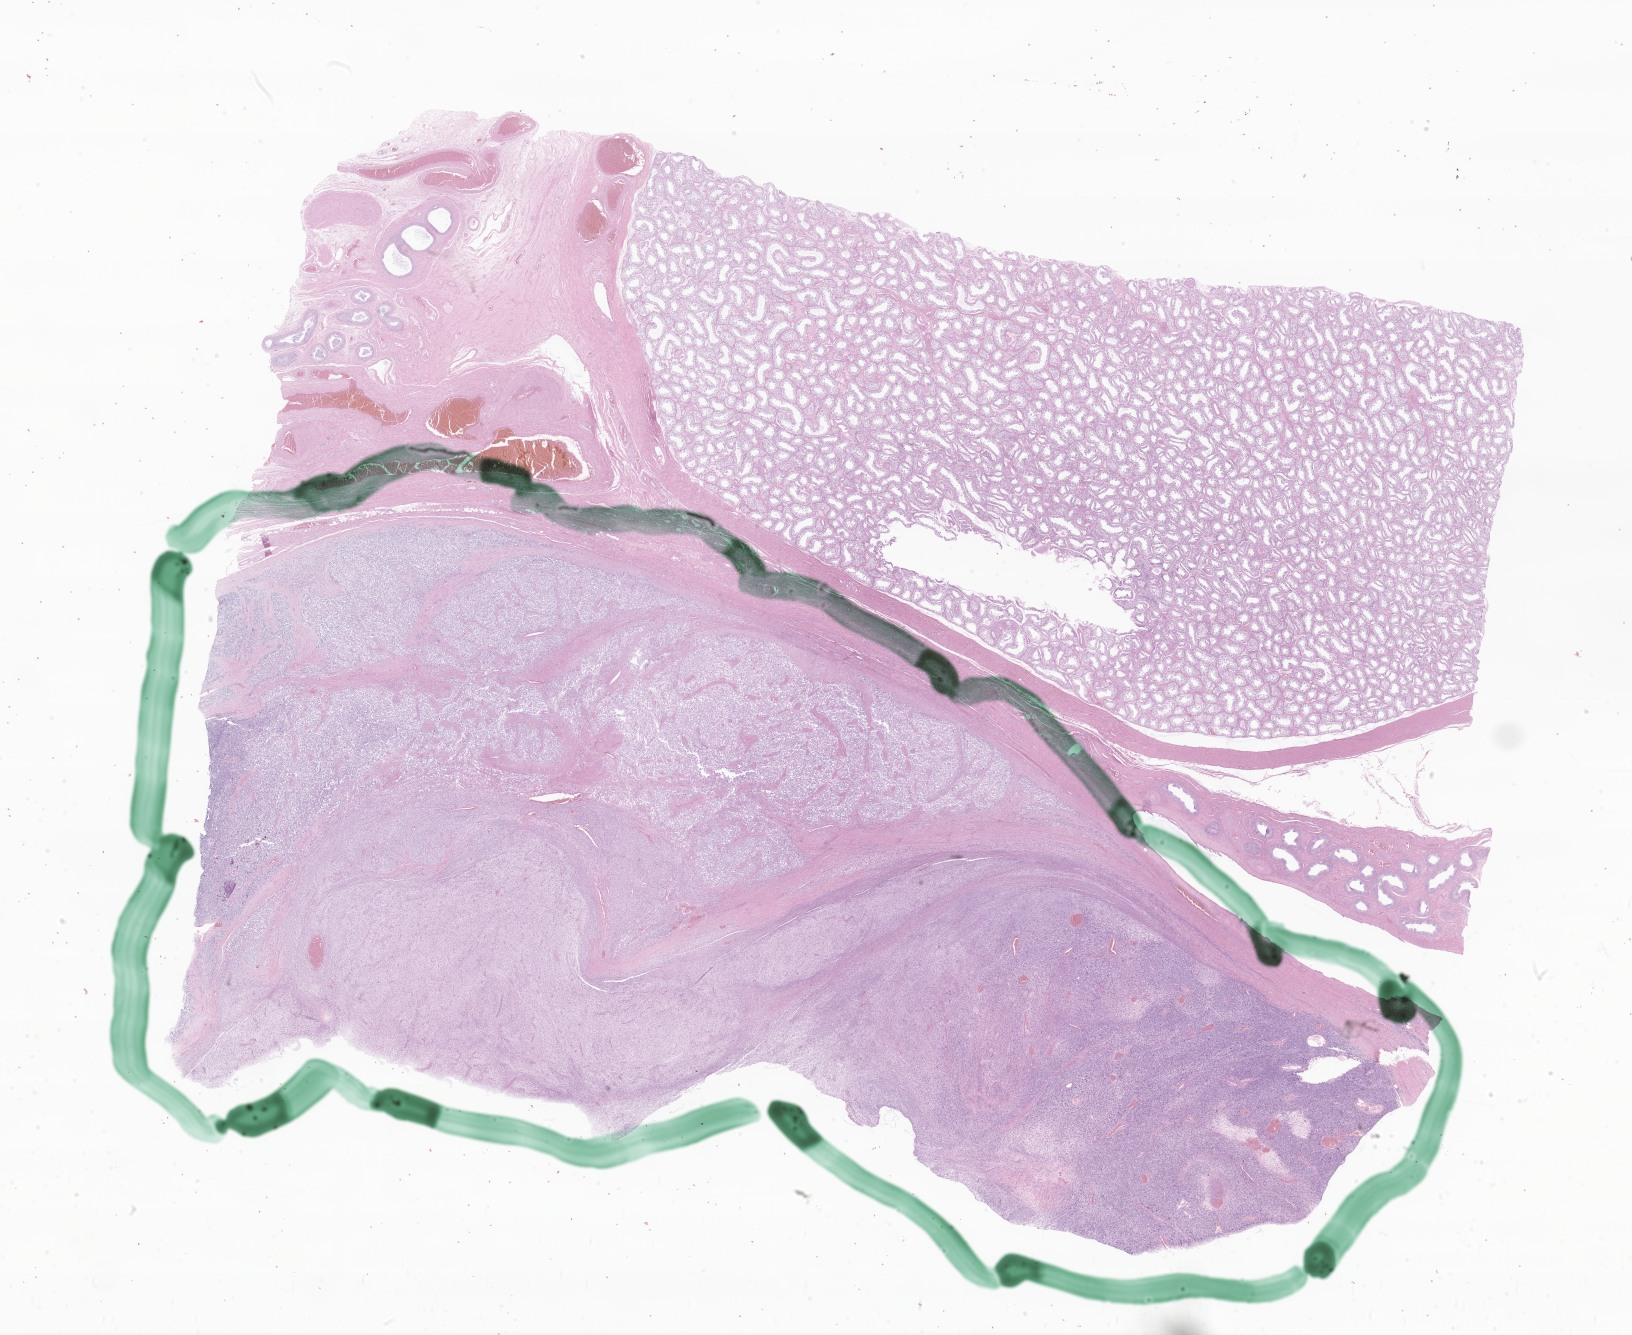
Whole-slide image, hematoxylin and eosin (H&E) stain of tumor tissue from the testis, a low-resolution overview of the entire scanned area, about 27.5 x 22.5 mm, formalin-fixed, paraffin-embedded (FFPE) tissue. Patient: male, age 176 months (14 years 8 months).
- diagnosis: Embryonal rhabdomyosarcoma, NOS